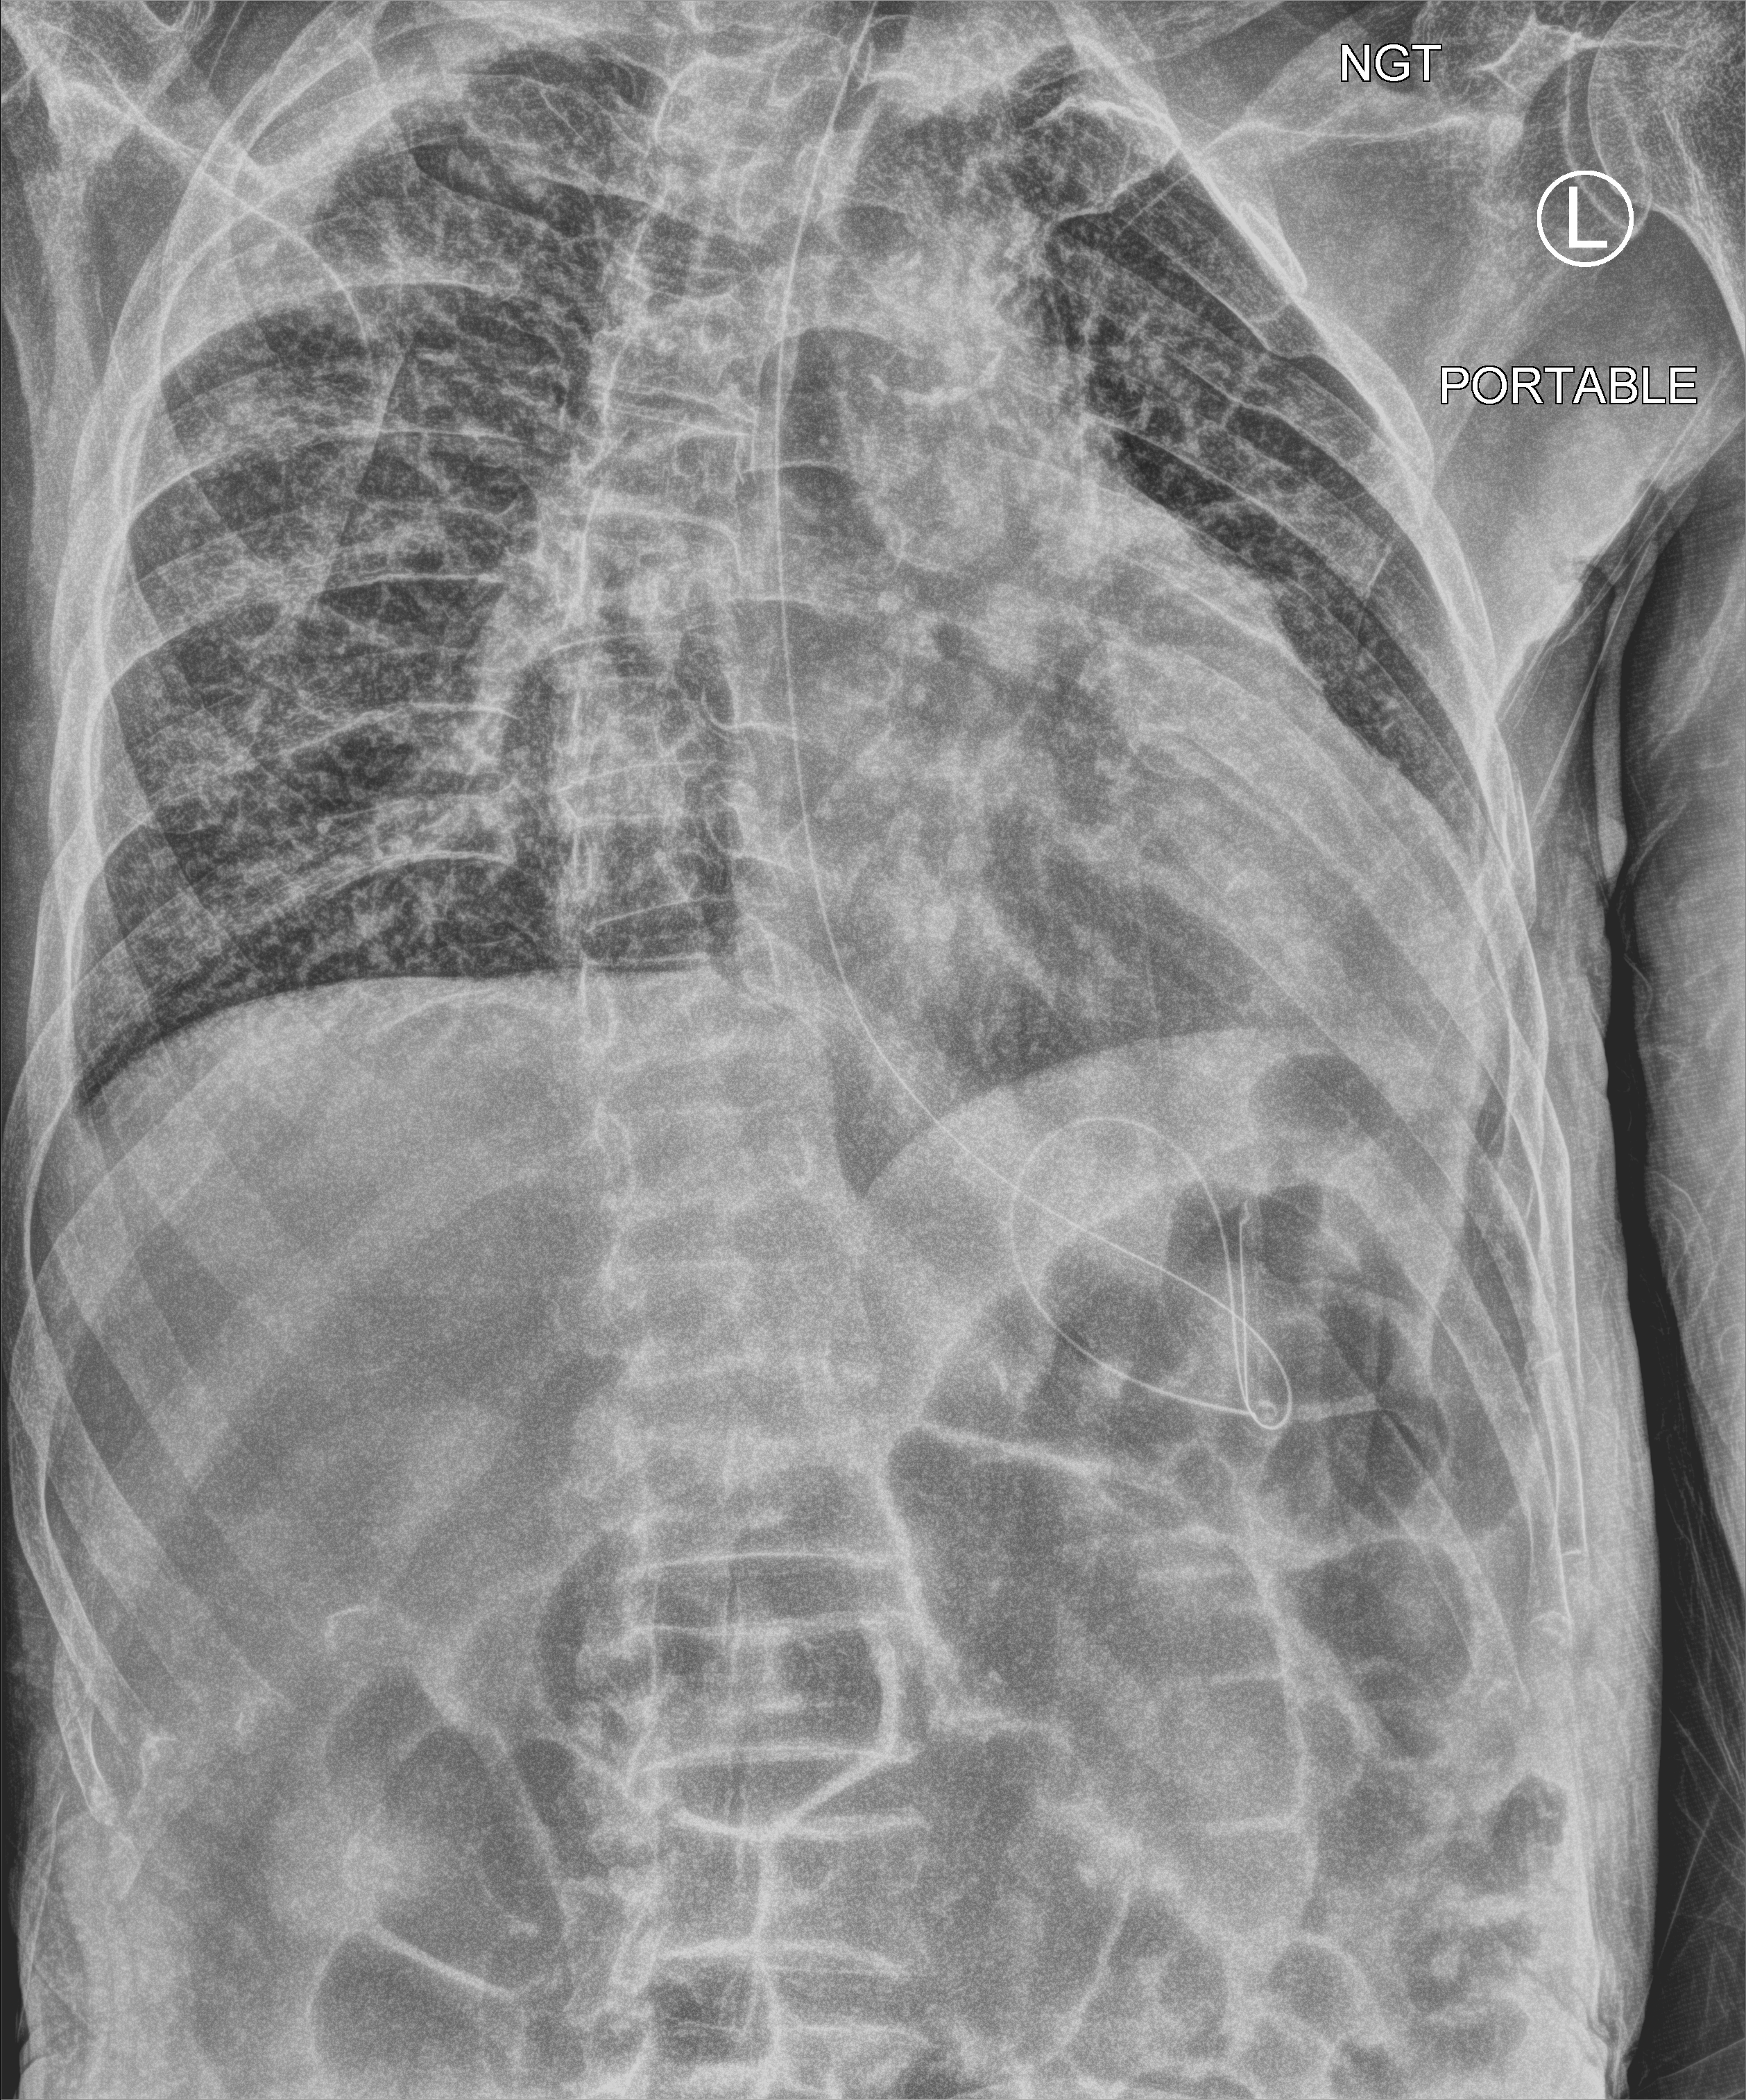
Bedside chest radiograph (computed radiography); anteroposterior (AP) projection. Patient hospitalised with COVID-19; male, aged 75–90 years.
Admission-level facts for this patient (not findings on this image; timing relative to this image not recorded): admitted to intensive care during this hospital stay: no.